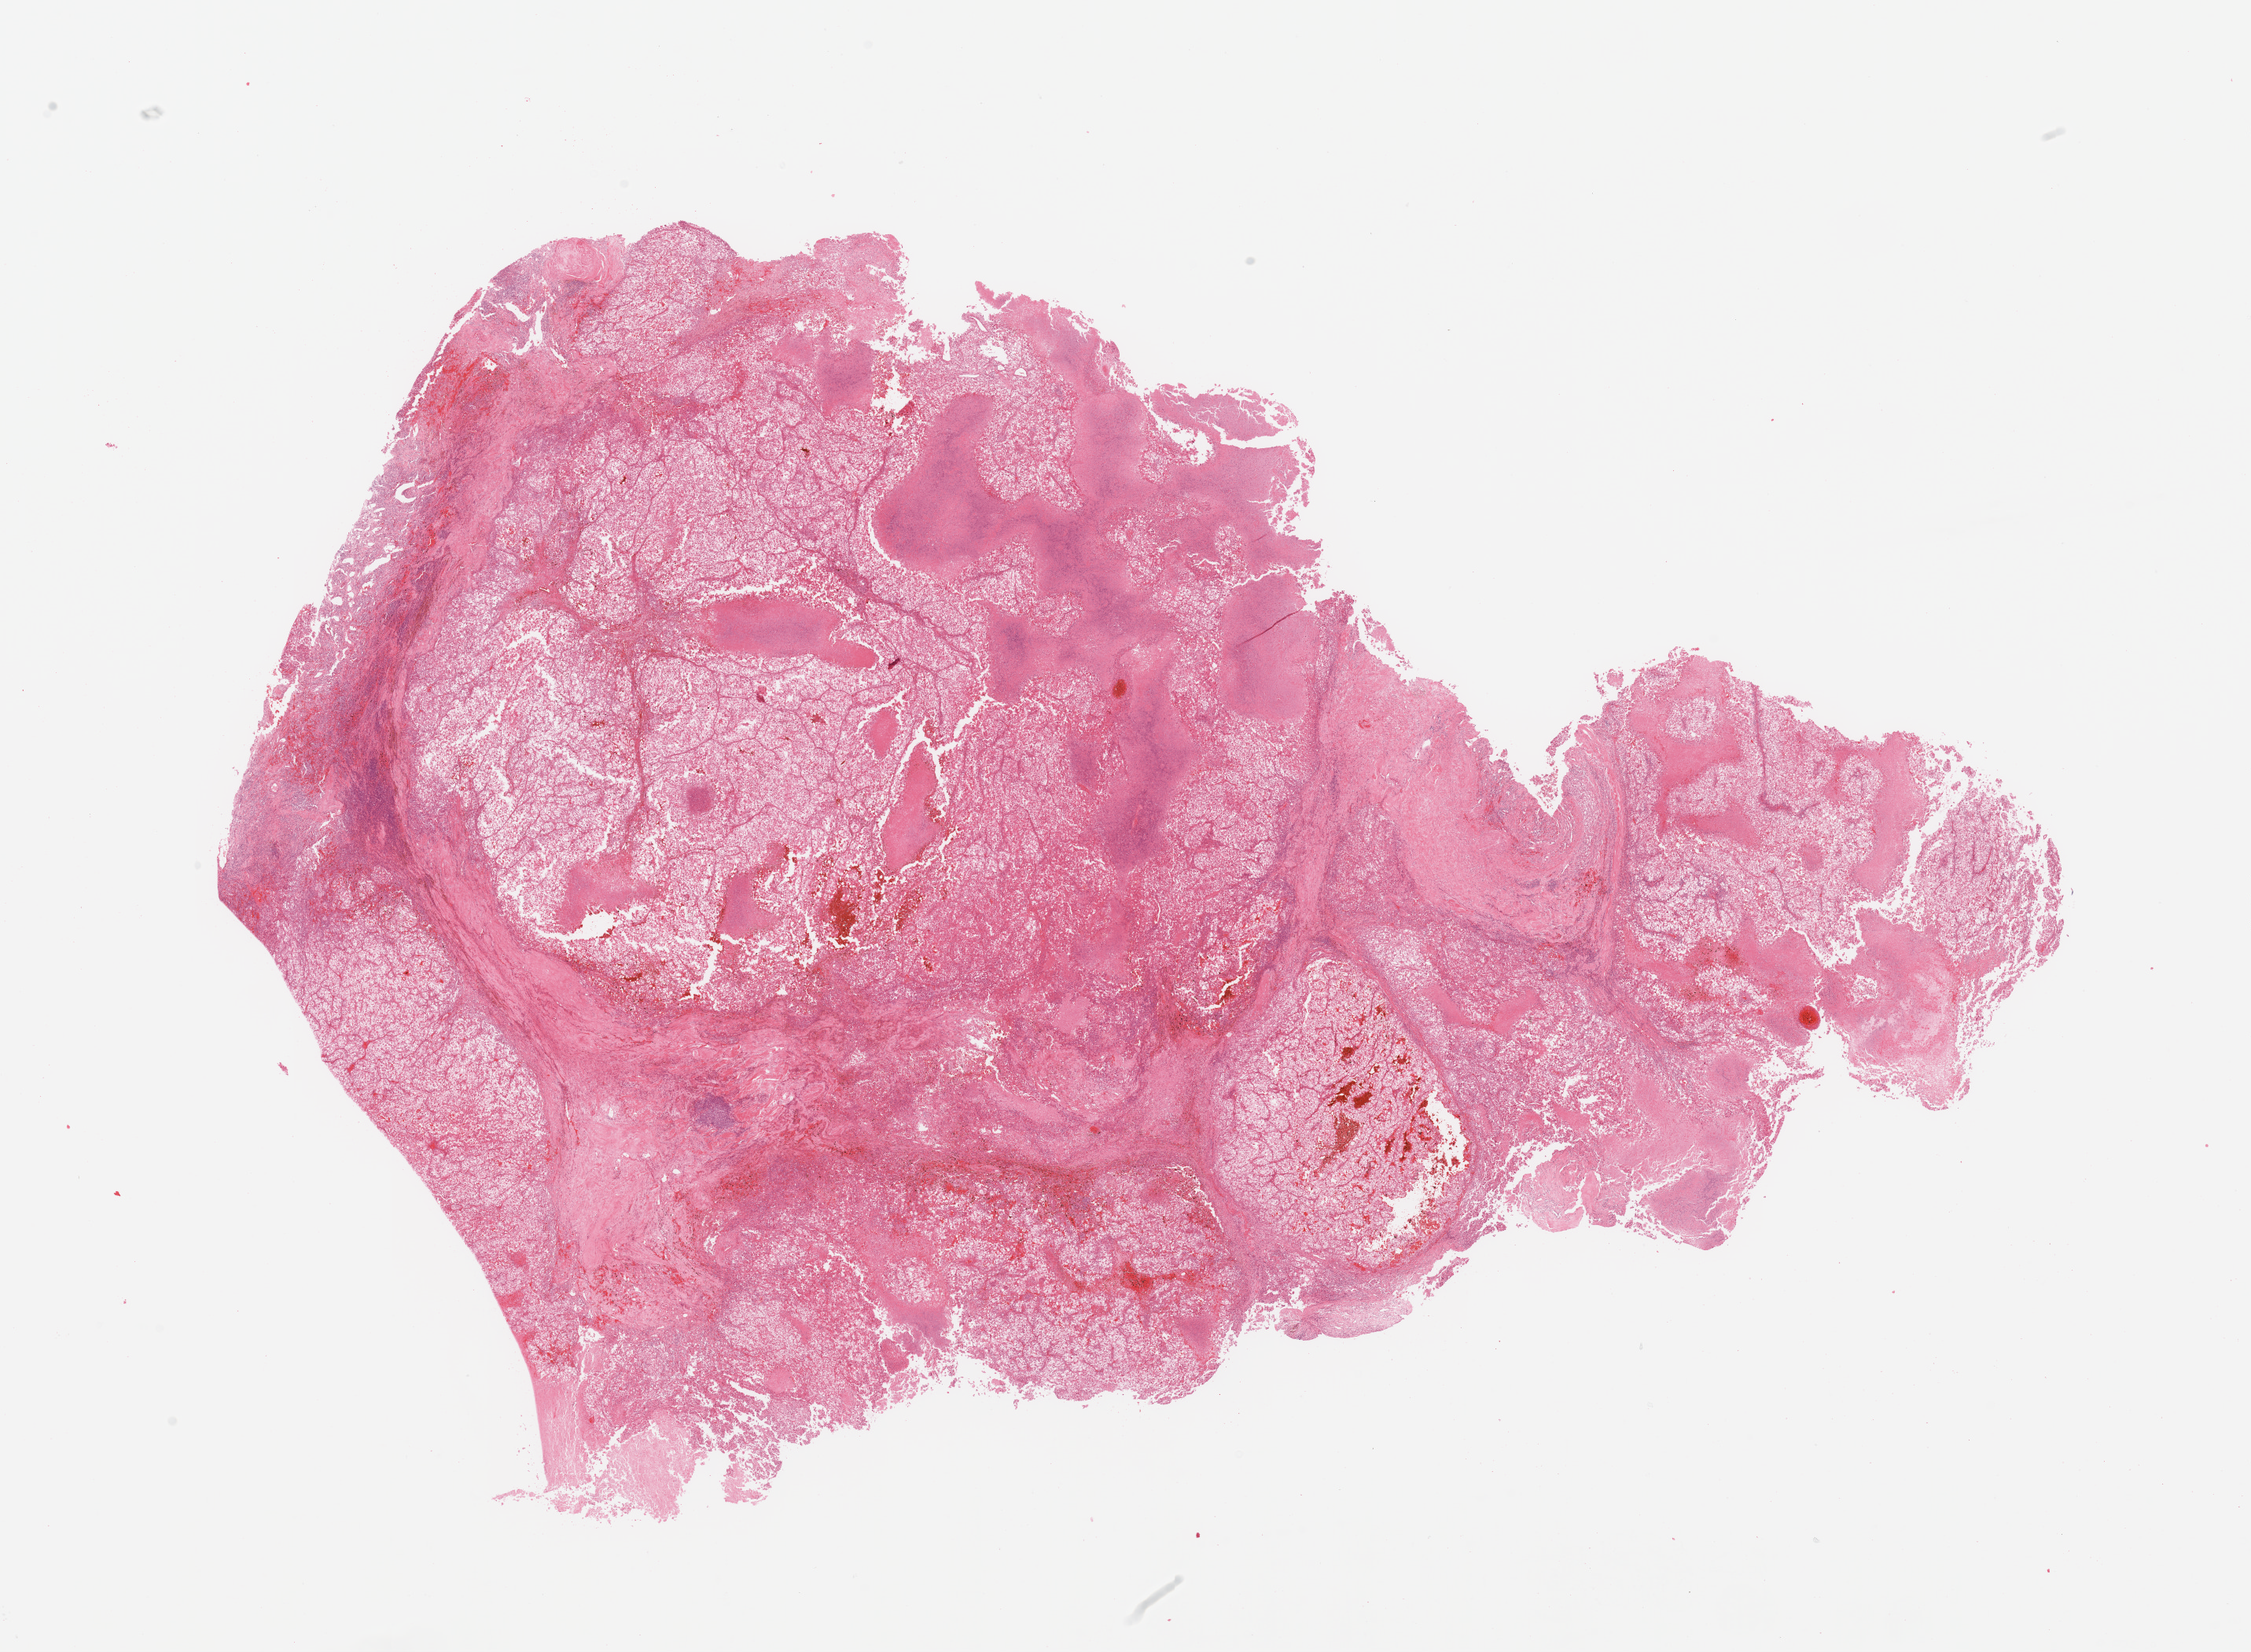
Digitized H&E tissue section (whole slide) — a low-resolution overview of the entire scanned area, about 22.6 x 16.6 mm (from a 20x scan), kidney, tumour tissue. Female, 52 y/o. Histologic grade: G2 (moderately differentiated).
Diagnosis: Renal cell carcinoma, NOS.